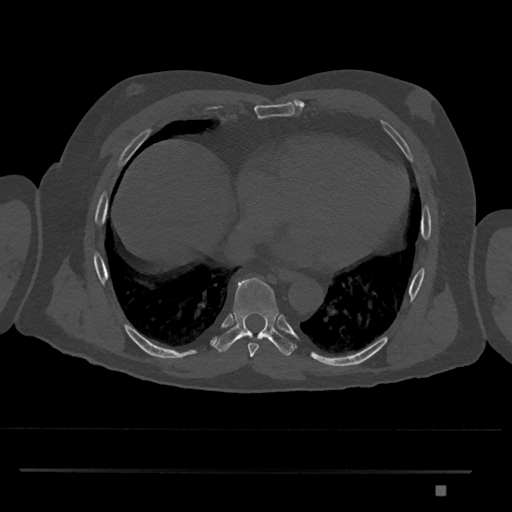
CT including the spine, one axial slice. Bone window (W 1800 / L 400 HU). 512 × 512 image matrix, field of view 429 × 429 mm. Male patient, age 65 years. Case-level facts recorded for this patient, not image findings: primary cancer: prostate.
Outlined on this slice (semi-automatic segmentation, software-assisted and operator-edited):
- T8 vertebra: bounding box (x1, y1, x2, y2) in pixels: (215, 276, 296, 357)